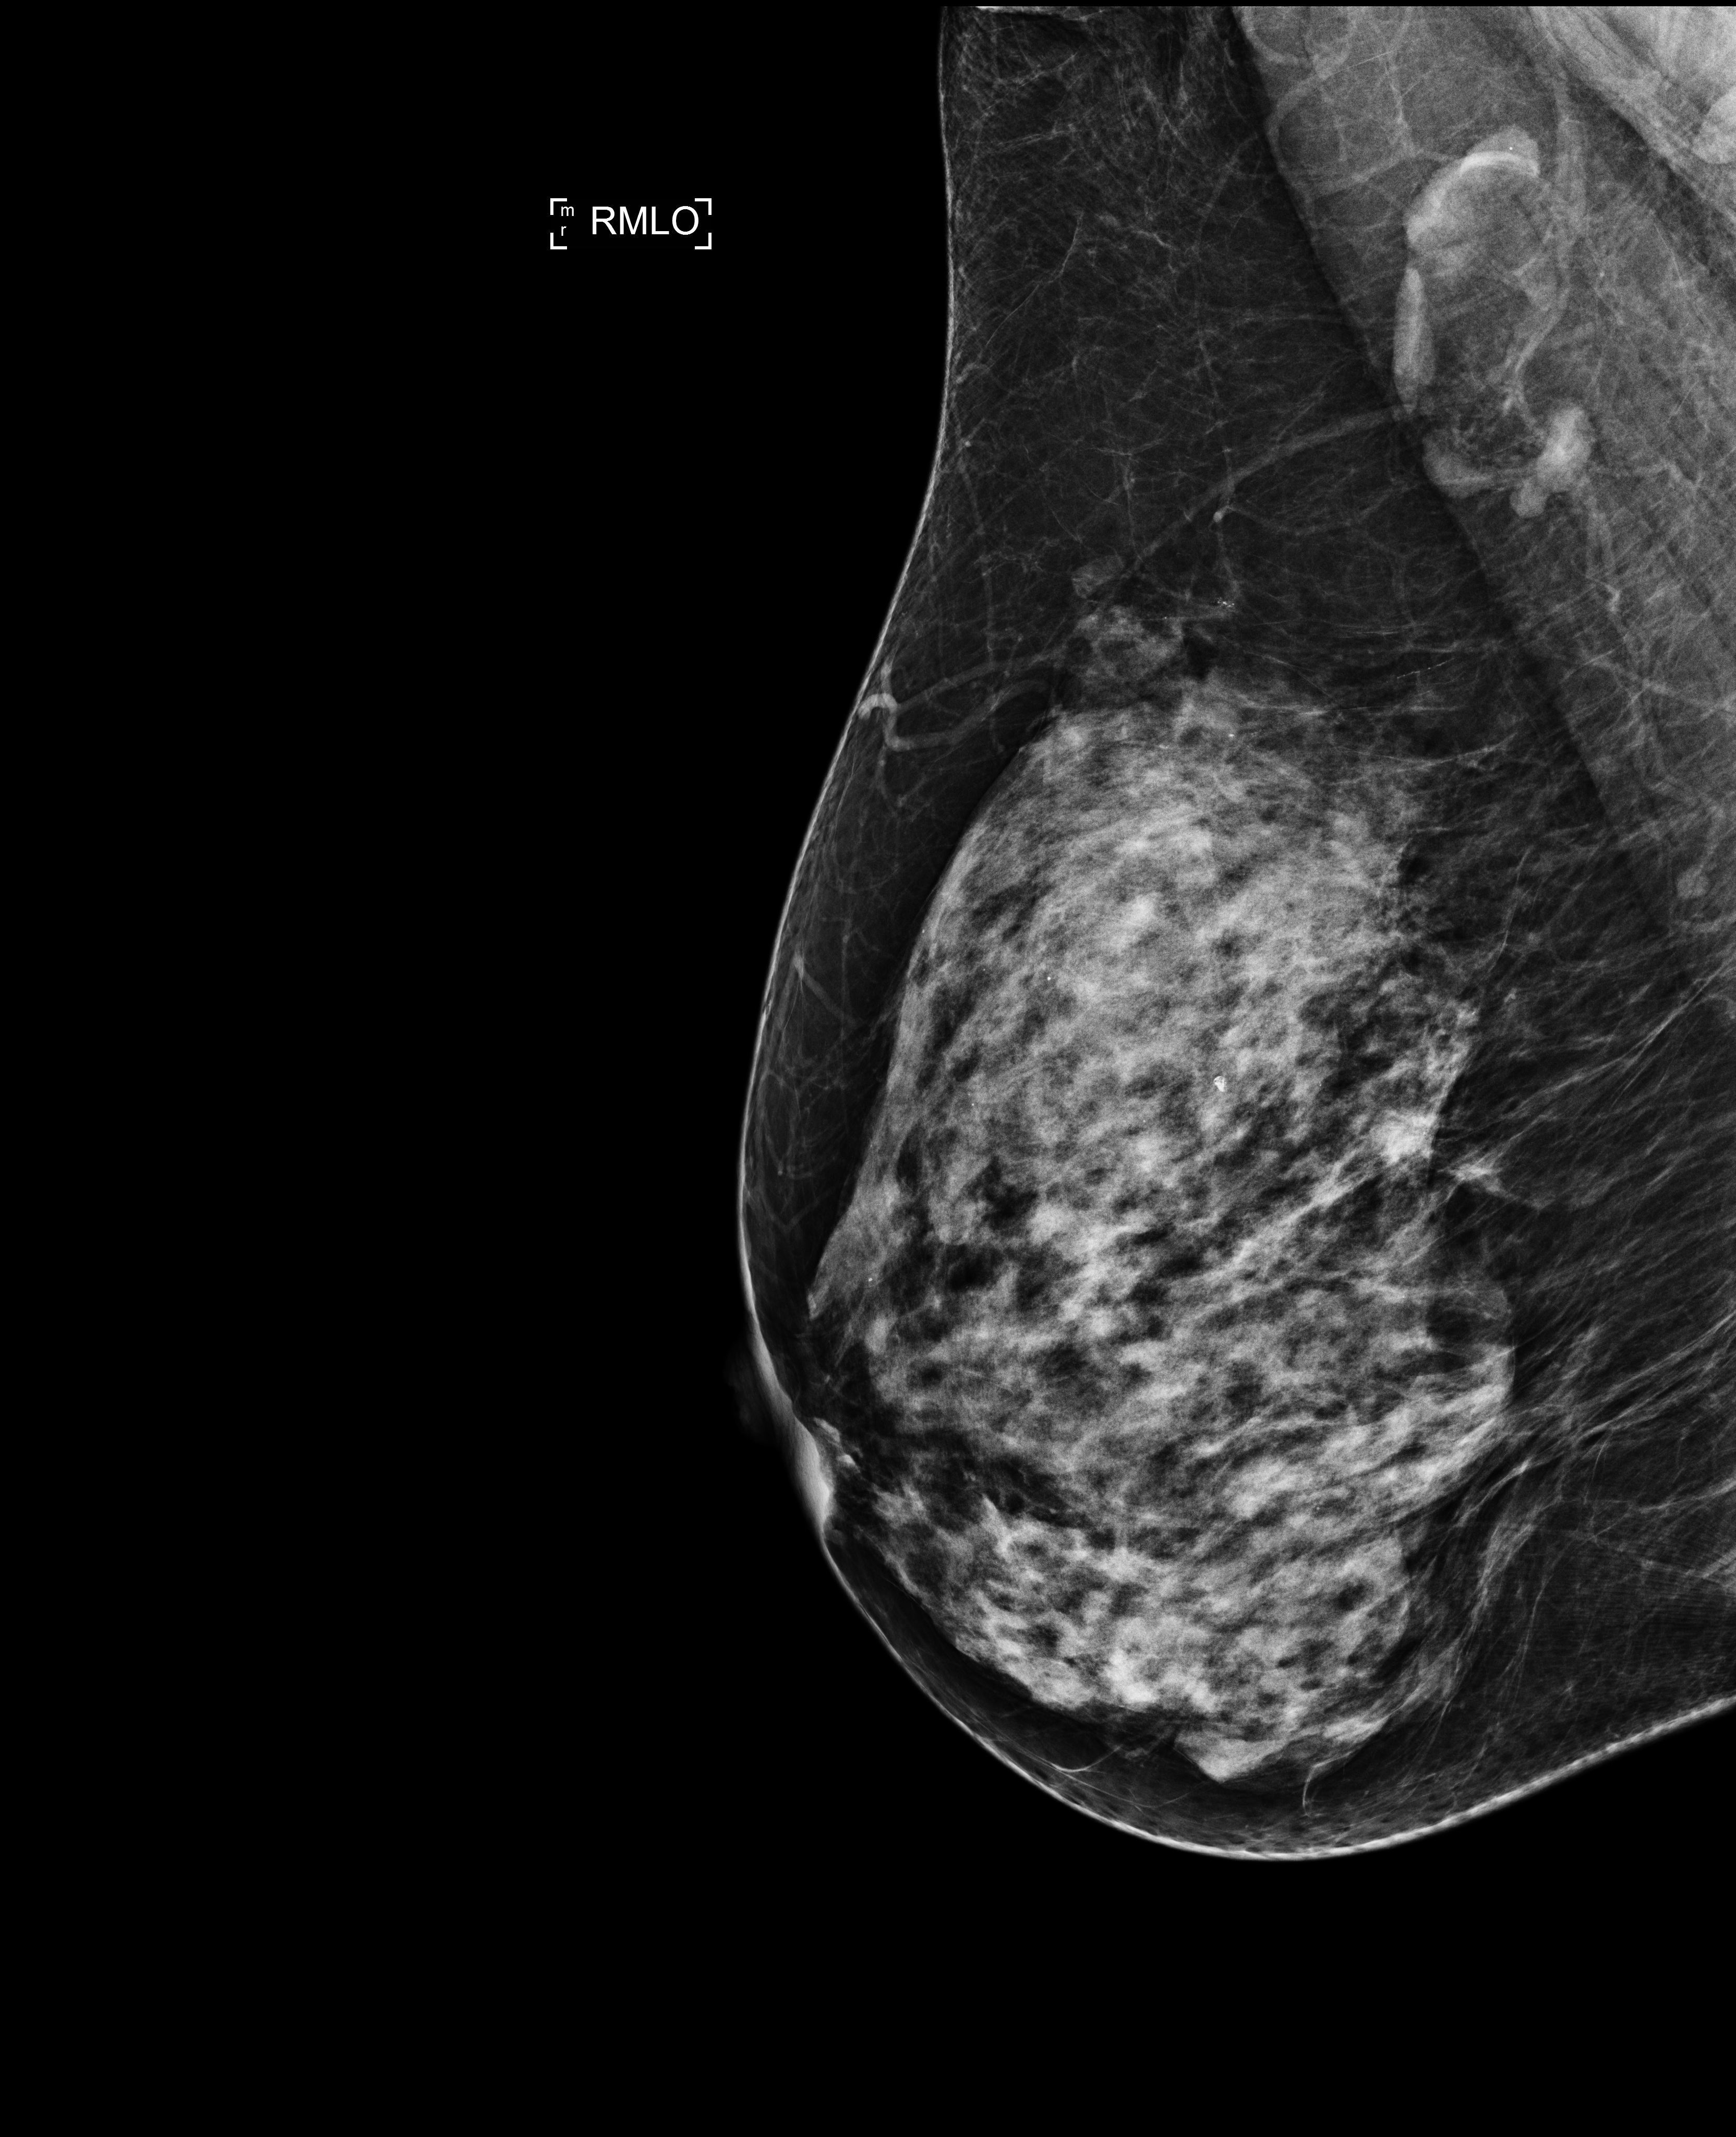
Annual screening mammography examination, system: Selenia Dimensions. Patient aged 57 years (female).
Image type: full-field digital mammogram. Breast: right. Projection: mediolateral oblique (MLO) view.